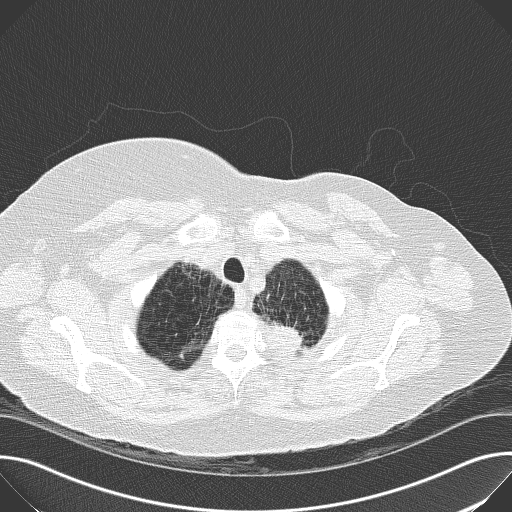
Axial slice from a low-dose chest CT screening exam, first (baseline) screen, lung window (W 1500 / L -600 HU), slice 151 of 169 in the series, 512 × 512 image matrix, field of view 380 × 380 mm. Female, age 56 years at enrolment. Current smoker at enrolment.
- Expert-annotated lung lesion, box from (x=256, y=303) to (x=322, y=365) px.
- Screening reader's record for this exam (one nodule recorded; not confirmed to be the boxed lesion): non-calcified nodule or mass ≥4 mm, left upper lobe, 19 × 17 mm, spiculated (stellate) margins, soft tissue attenuation.
- Official screen result: positive, change unspecified: nodule(s) >= 4 mm or enlarging nodule(s), mass(es), or other non-specific abnormalities suspicious for lung cancer.